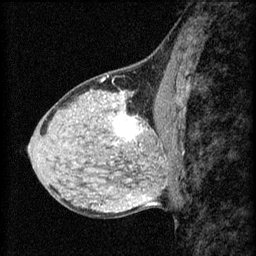
Breast MRI (dynamic contrast-enhanced), one sagittal slice; slice 27 of 60 in the series (ordered by position); 3 images stored at this slice position (order not interpretable as contrast timing); 1.5 T; TE 4.2 ms, TR 8.2 ms; 256 × 256 image matrix, field of view 180 × 180 mm. Patient: female, 40 years.
Annotated regions visible in this slice (semi-automatic segmentation, software-assisted and operator-edited):
- analysis volume of interest (the breast-tissue region the enhancement analysis was run in; not a lesion): bounding box (x1, y1, x2, y2) in pixels: (108, 108, 167, 159)
- tumour enhancement mask (voxels above the 70 % enhancement threshold inside the analysis volume of interest): (114, 116, 145, 147)